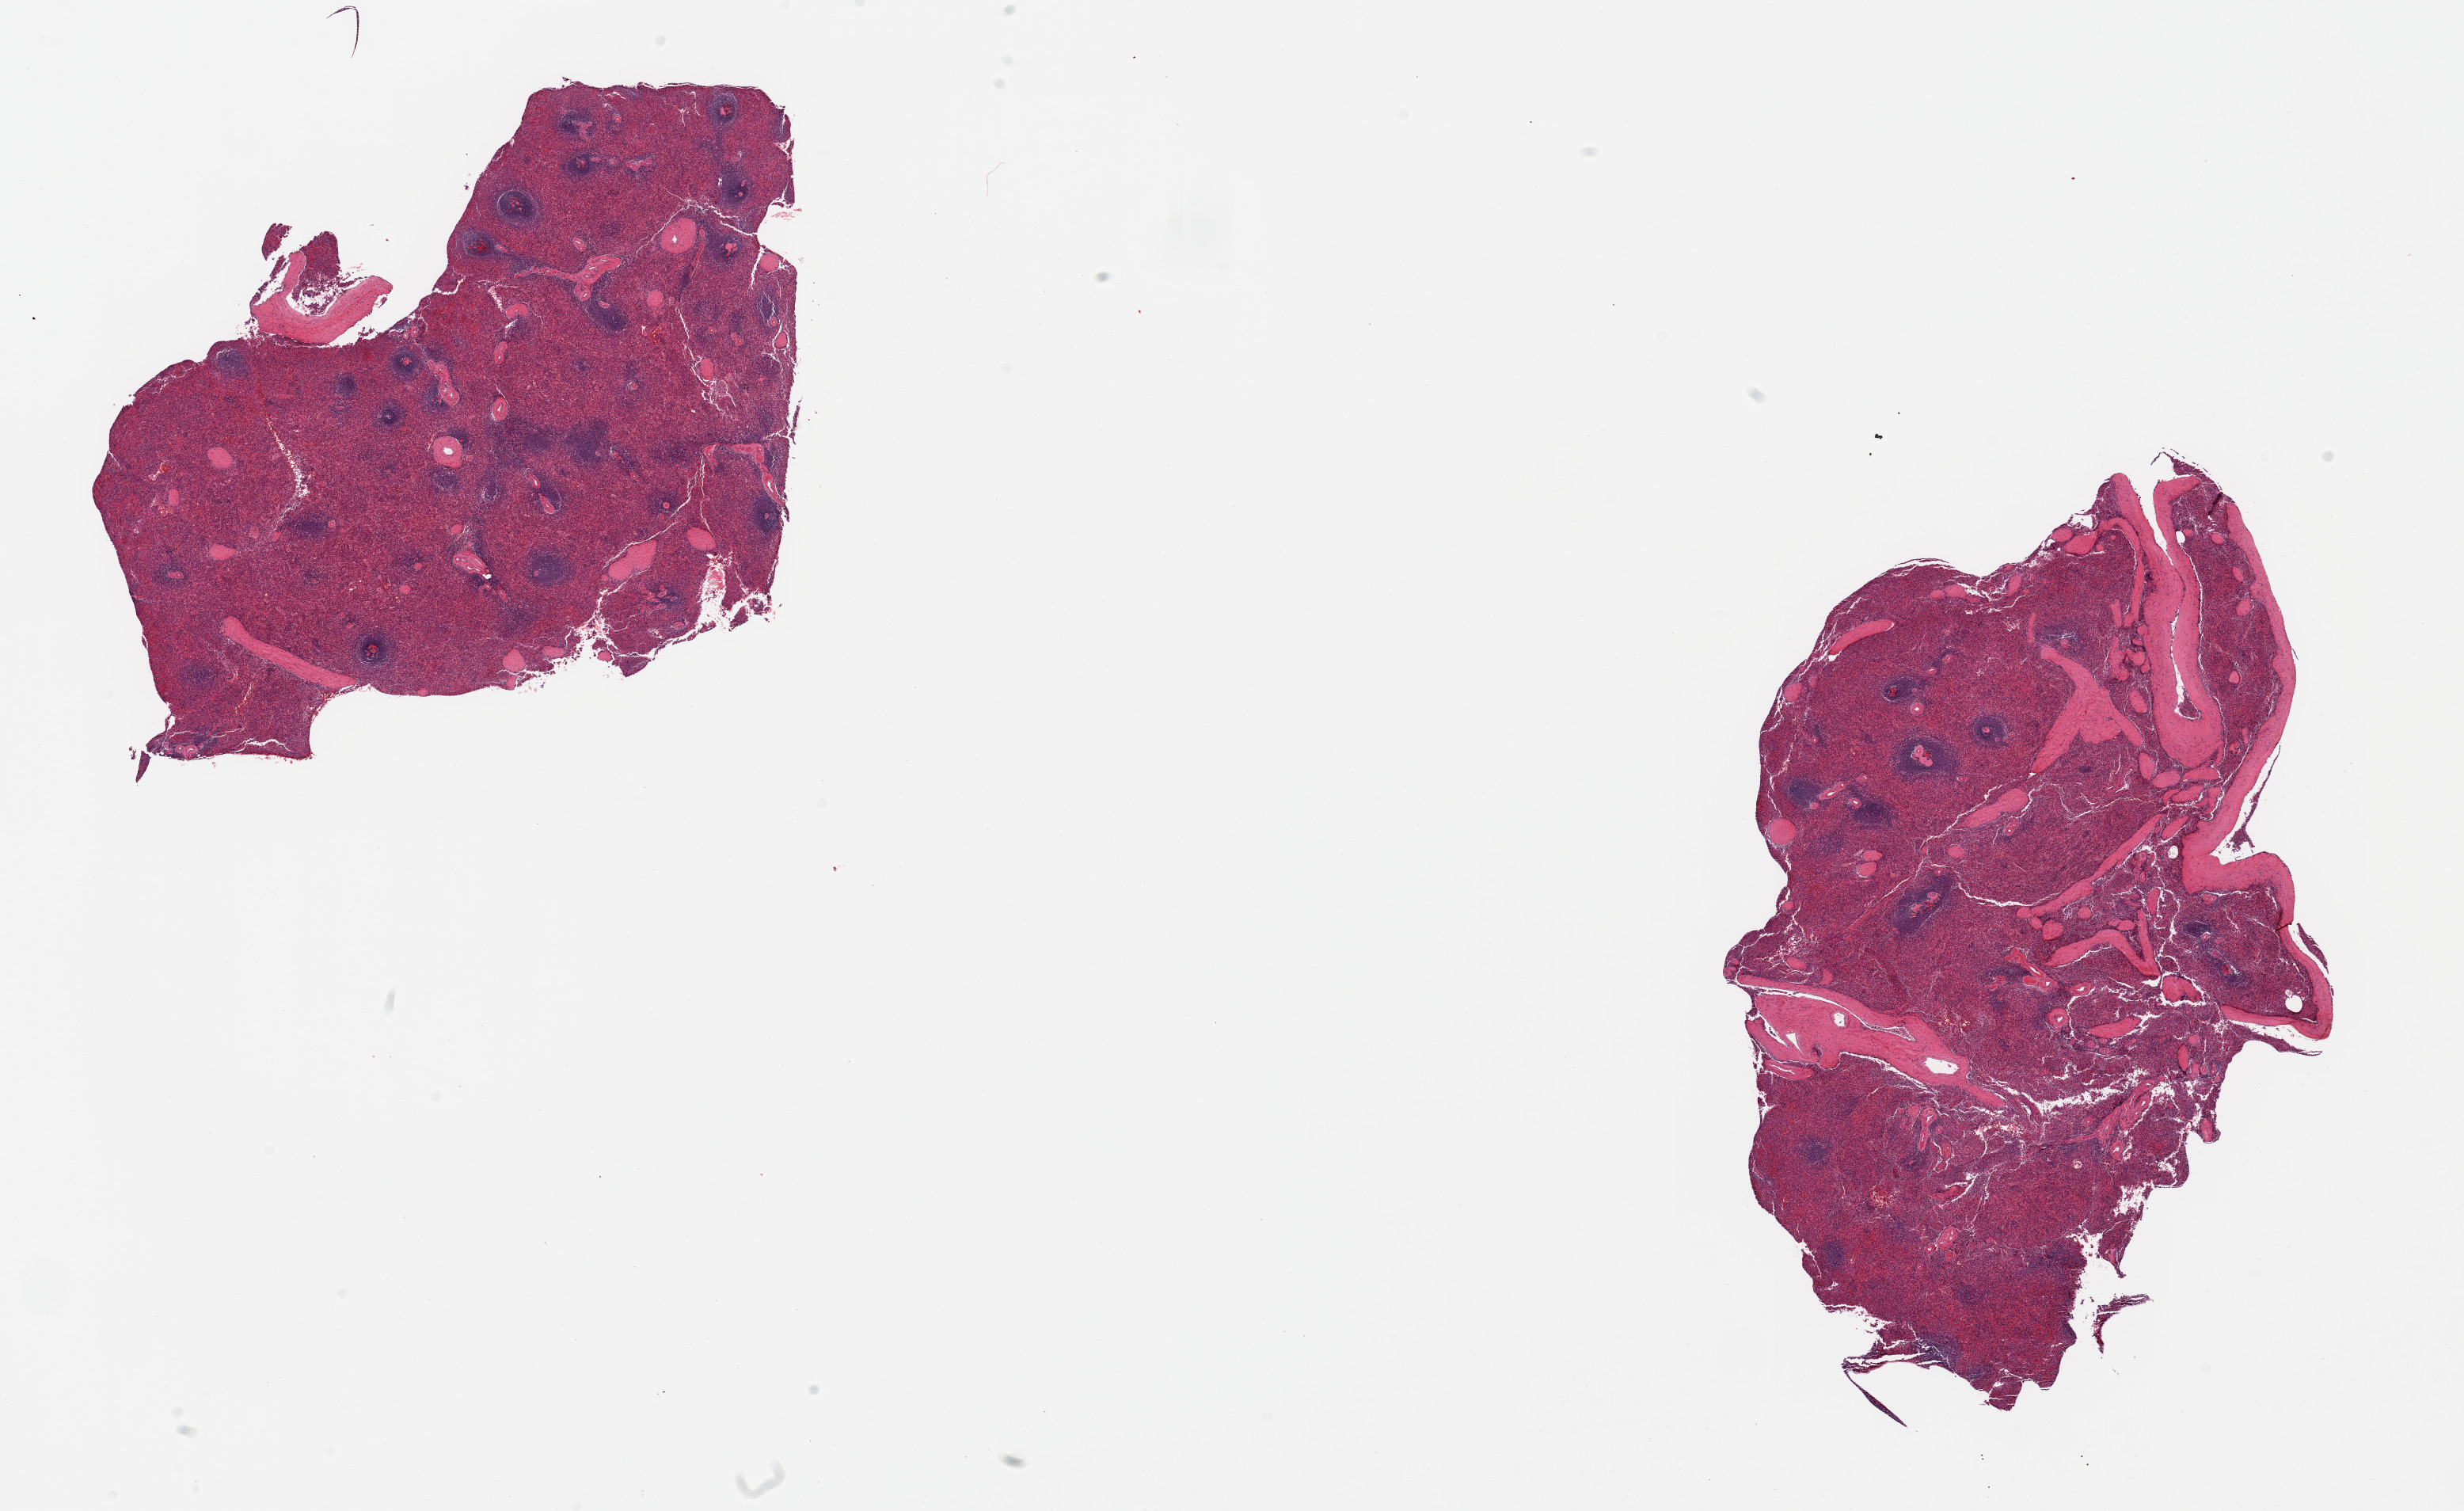
Digitized haematoxylin and eosin-stained section, low-resolution overview of the scanned area, about 24.6 x 15.1 mm (slide scanned at 20x), PAXgene-fixed, paraffin-embedded tissue, target tissue: spleen, tissue donor sample. Donor sex: male.
Pathologist's review note for this sample: 2 pieces, minimal congestion.